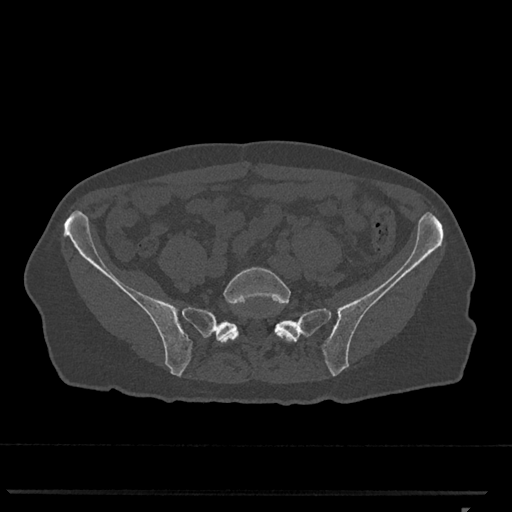
CT including the spine, one axial slice. Position 125 of 793 along the scan axis. 120 kVp. Bone window (W 1800 / L 400 HU). 0.5 mm slice thickness. 512 × 512 image matrix, field of view 380 × 380 mm. Patient: female, 62 years. From the clinical record (not read from this slice): primary cancer: renal.
Outlined on this slice (semi-automatically segmented with operator editing):
- L5 vertebra: bounding box [x1, y1, x2, y2] px = [219, 267, 297, 343]